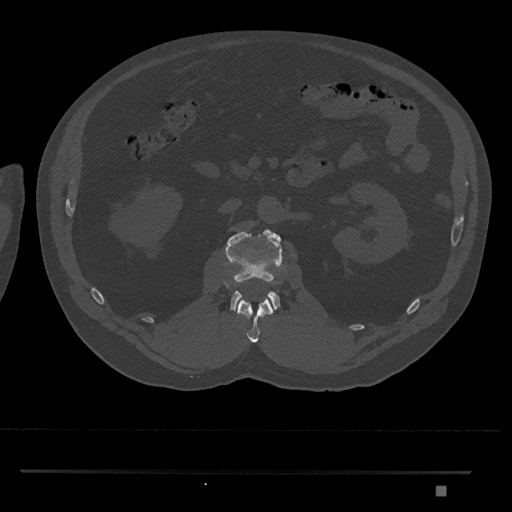
CT including the spine, one axial slice; position 787 of 1134 along the scan axis; reconstruction kernel Br40s/3; 120 kVp; bone window (W 1800 / L 400 HU); 0.5 mm slice thickness; 512 × 512 image matrix, field of view 429 × 429 mm. Male patient, age 65 years. From the clinical record (not read from this slice): primary cancer: prostate.
Structures marked on this image (semi-automatically segmented with operator editing):
- L1 vertebra: box from (x=237, y=297) to (x=275, y=343) px
- L2 vertebra: (x=225, y=229)–(x=282, y=311)